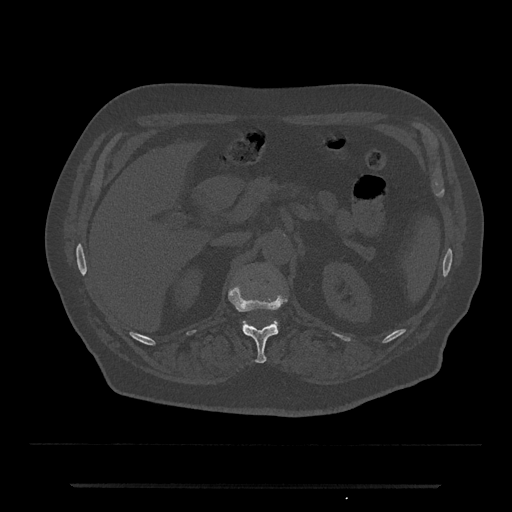
CT including the spine, one axial slice. Position 578 of 797 along the scan axis. 120 kVp. Bone window (W 1800 / L 400 HU). 0.5 mm slice thickness. 512 × 512 image matrix. Patient: male, 80 years. From the clinical record (not read from this slice): primary cancer: prostate.
Outlined on this slice (semi-automatically segmented with operator editing):
- L1 vertebra: bounding box <241,263,279,328> (left, top, right, bottom; pixels)
- T12 vertebra: <229,288,286,363>